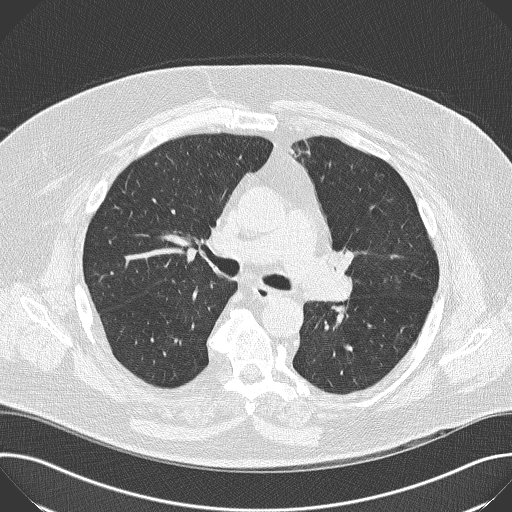
Chest CT (low-dose screening protocol), one axial image. First (baseline) screen. Lung window (W 1500 / L -600 HU). 2 mm slice thickness. Lung (sharp) reconstruction kernel (B50f). Slice 58 of 138 in the series. 512 × 512 image matrix. Male, age 68 years at enrolment. Former smoker at enrolment.
- Expert reader's lesion annotation, bounding box [x1, y1, x2, y2] px = [318, 234, 369, 283].
- The screening reader recorded 2 non-calcified nodules or masses ≥4 mm on this exam (left lower lobe, right lower lobe); which of them this box marks is not recorded.
- Official screen result: positive, change unspecified: nodule(s) >= 4 mm or enlarging nodule(s), mass(es), or other non-specific abnormalities suspicious for lung cancer.
- Lung cancer was diagnosed 638 days after this screen: squamous cell carcinoma, NOS, left upper lobe, poorly differentiated (G3), stage IIB (AJCC 6th edition), 35 mm at pathology.